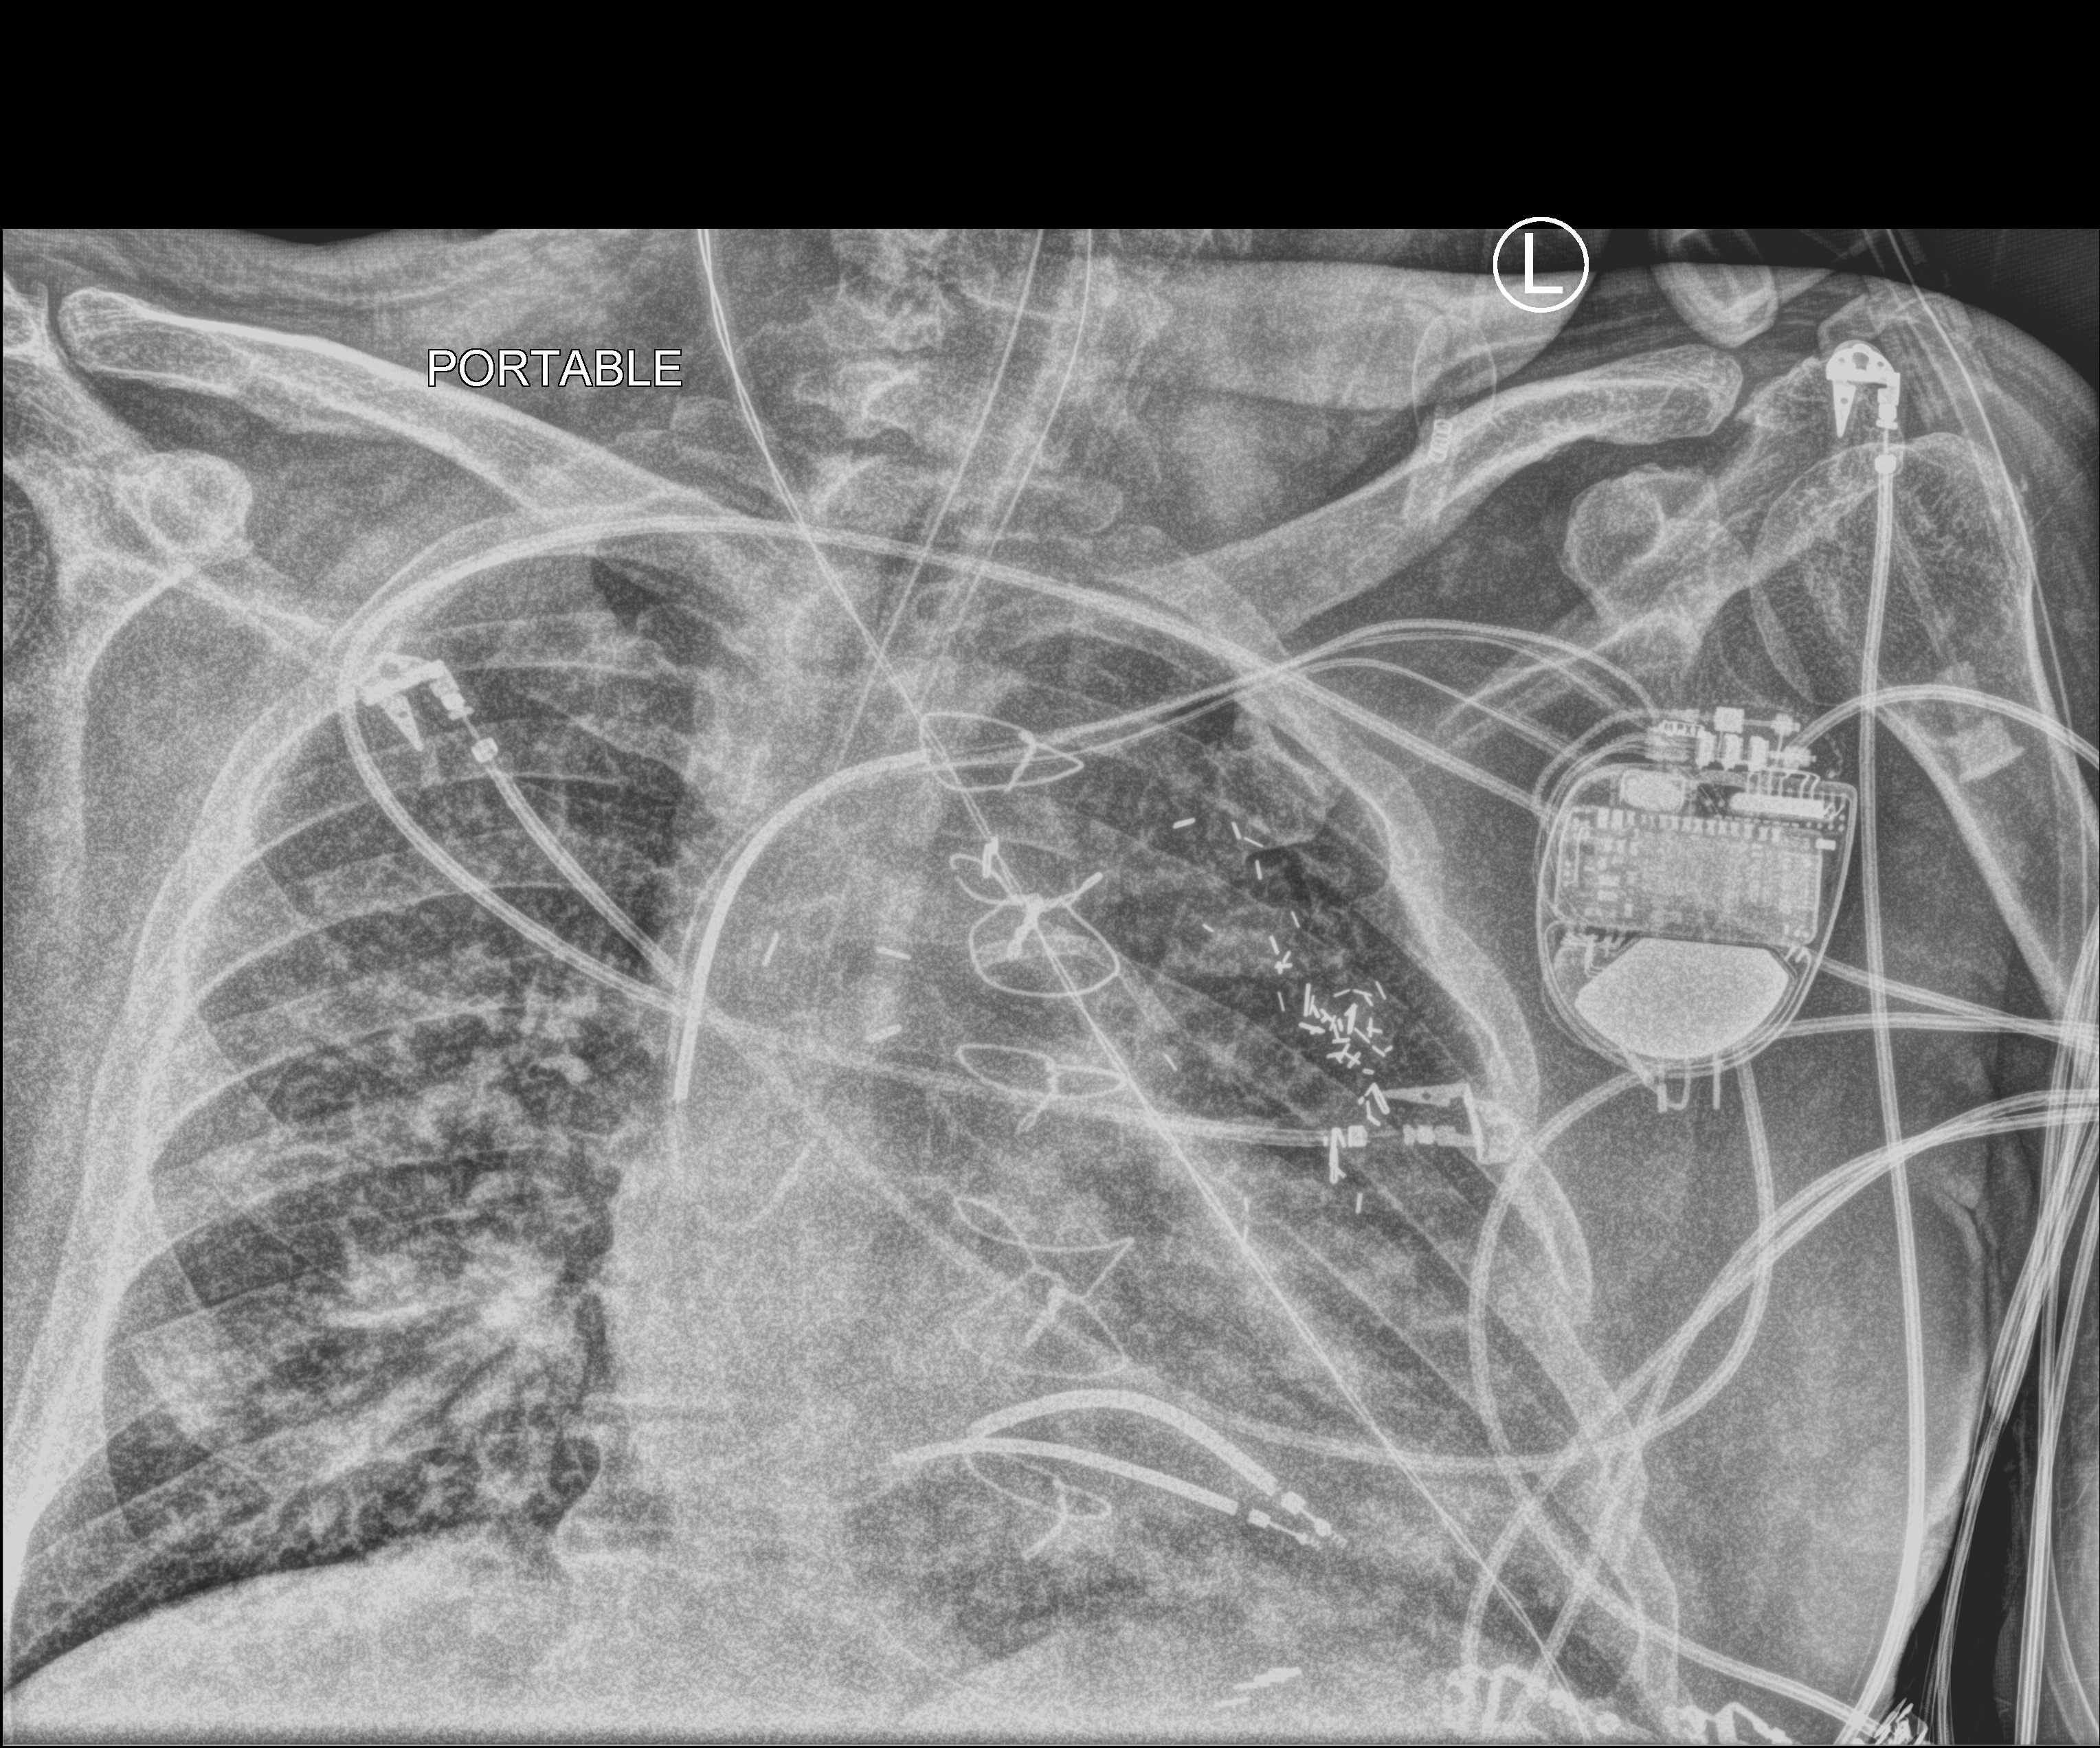
Chest X-ray (portable); anteroposterior (AP) projection. Male patient hospitalised with COVID-19, age 60–74 years.
Admission-level facts for this patient (not findings on this image; timing relative to this image not recorded):
- other chronic lung disease (admission record): no
- admitted to intensive care during this hospital stay: yes